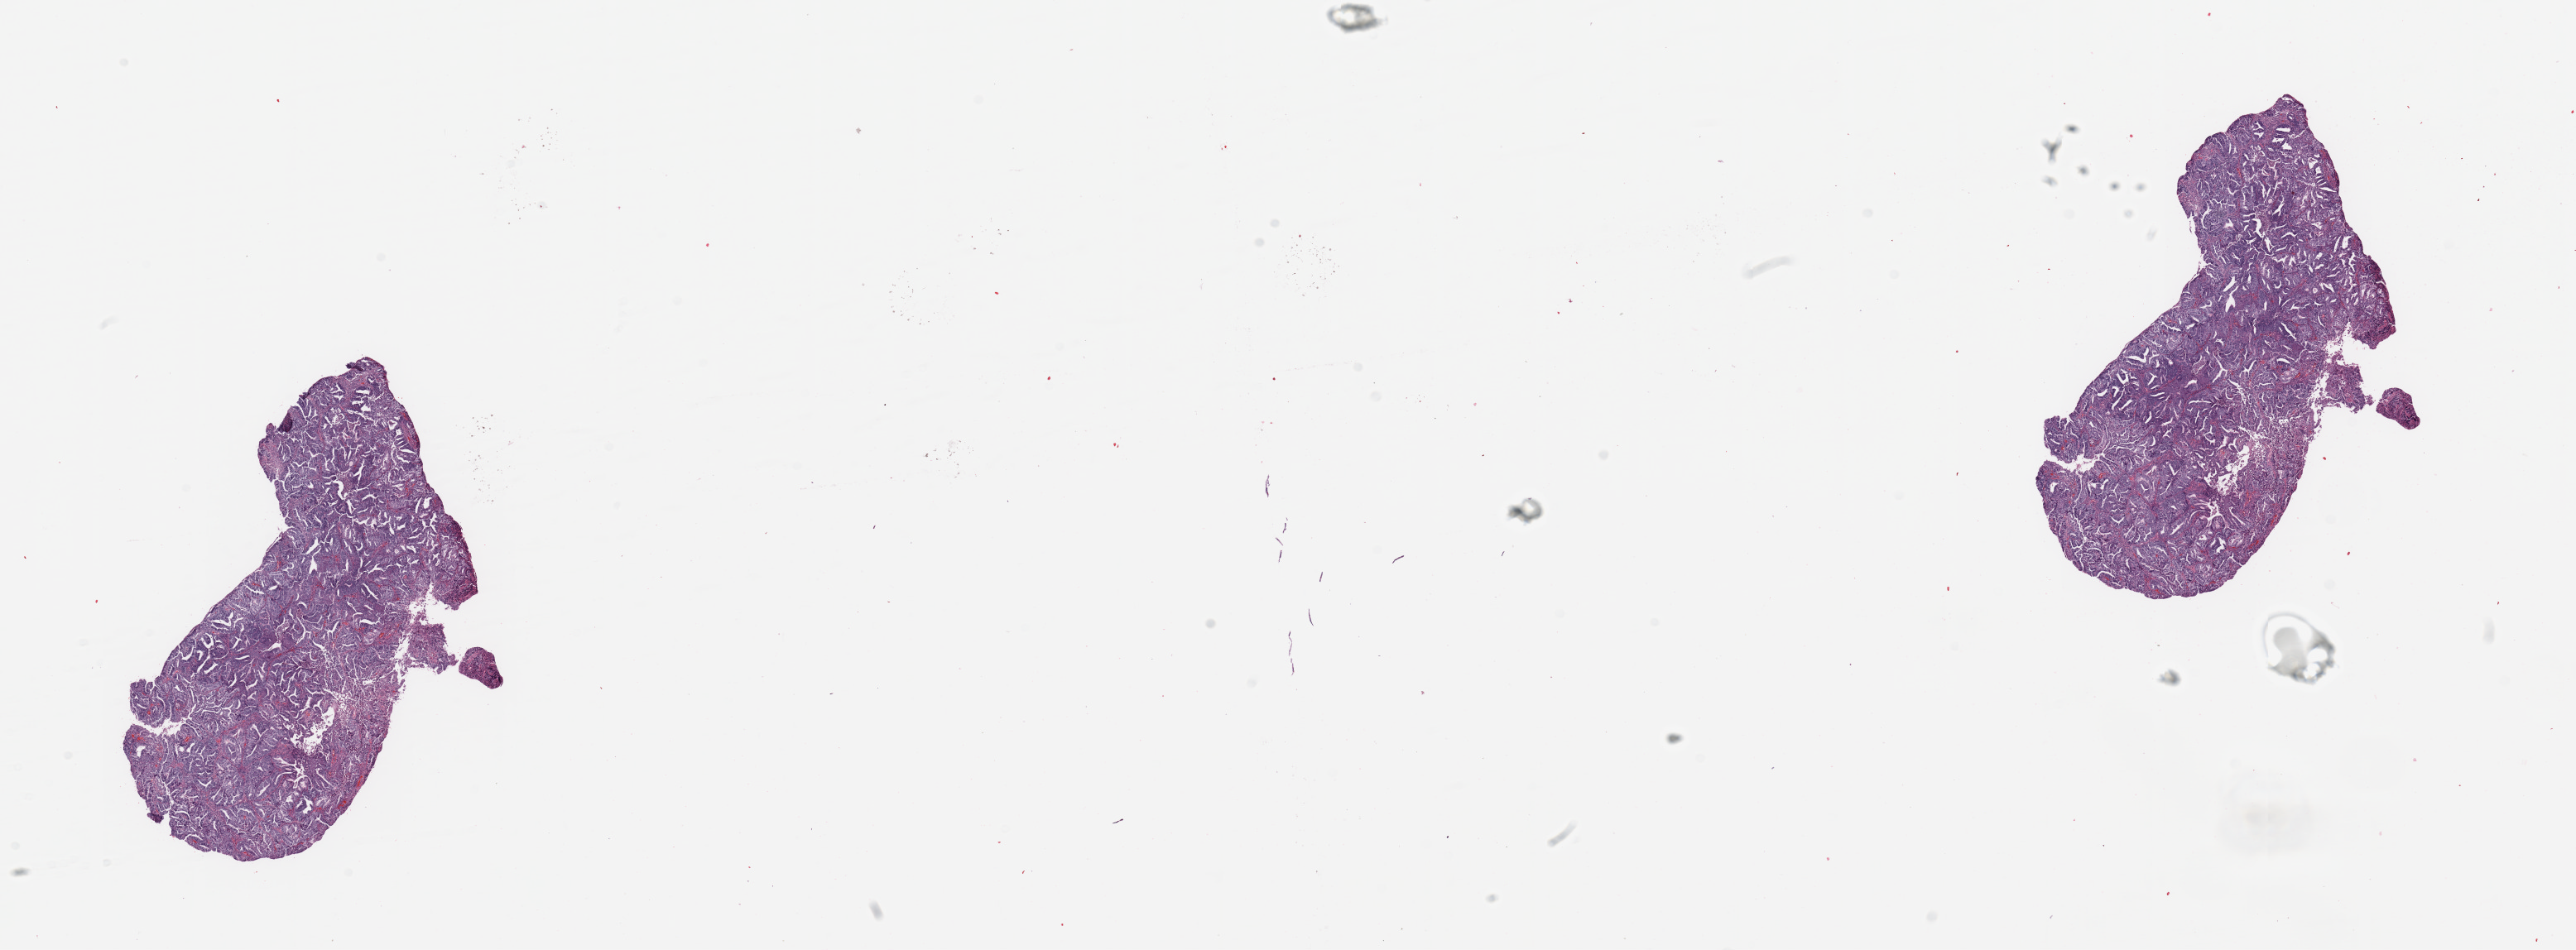
Whole-slide histology image, Hematoxylin and eosin (H&E) stained, shown as a low-resolution overview of the whole scanned area (about 24.6 x 9.1 mm, acquisition: 20x scan), tumour tissue sample, sampled site: uterus. Female, 61 y/o. Histologic grade: G2 (moderately differentiated). Composition of this section per pathologist review: tumour nuclei 90%, necrosis 2%.
• diagnosis: Endometrioid adenocarcinoma, NOS
• AJCC pathologic stage: III